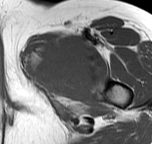
MRI of an extremity soft-tissue mass, one axial slice. Position 44 of 57 along the scan axis. MR volume resampled by the dataset authors to the PET/CT grid (not the native acquisition matrix). 3.27 mm slice thickness. 152 × 144 image matrix, field of view 148 × 141 mm. Female patient. From the clinical record (not read from this slice): histological type: pleiomorphic leiomyosarcoma; grade: intermediate; site of the primary tumour: left thigh.
Structures marked on this image (expert contour drawn on MRI and transferred to this co-registered scan by the dataset authors):
- gross tumour volume including surrounding oedema: bounding box [x1, y1, x2, y2] px = [25, 34, 94, 88]
- gross tumour volume (mass): [29, 35, 94, 88]